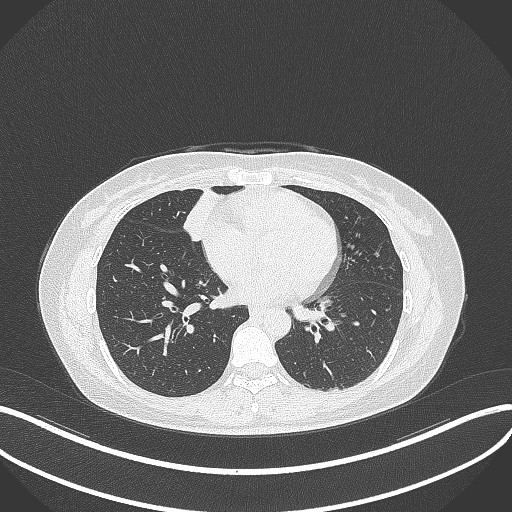
Chest CT, one axial slice; reconstruction kernel B70f; 120 kVp; lung window (W 1500 / L -600 HU); 512 × 512 image matrix. Patient: female, 43 years. From the clinical record (not read from this slice): clinical TNM (as recorded): T1c N3 M1.
Structures marked on this image (bounding box drawn by a radiologist):
- lung tumour (recorded histology: adenocarcinoma): box from (x=185, y=187) to (x=223, y=246) px